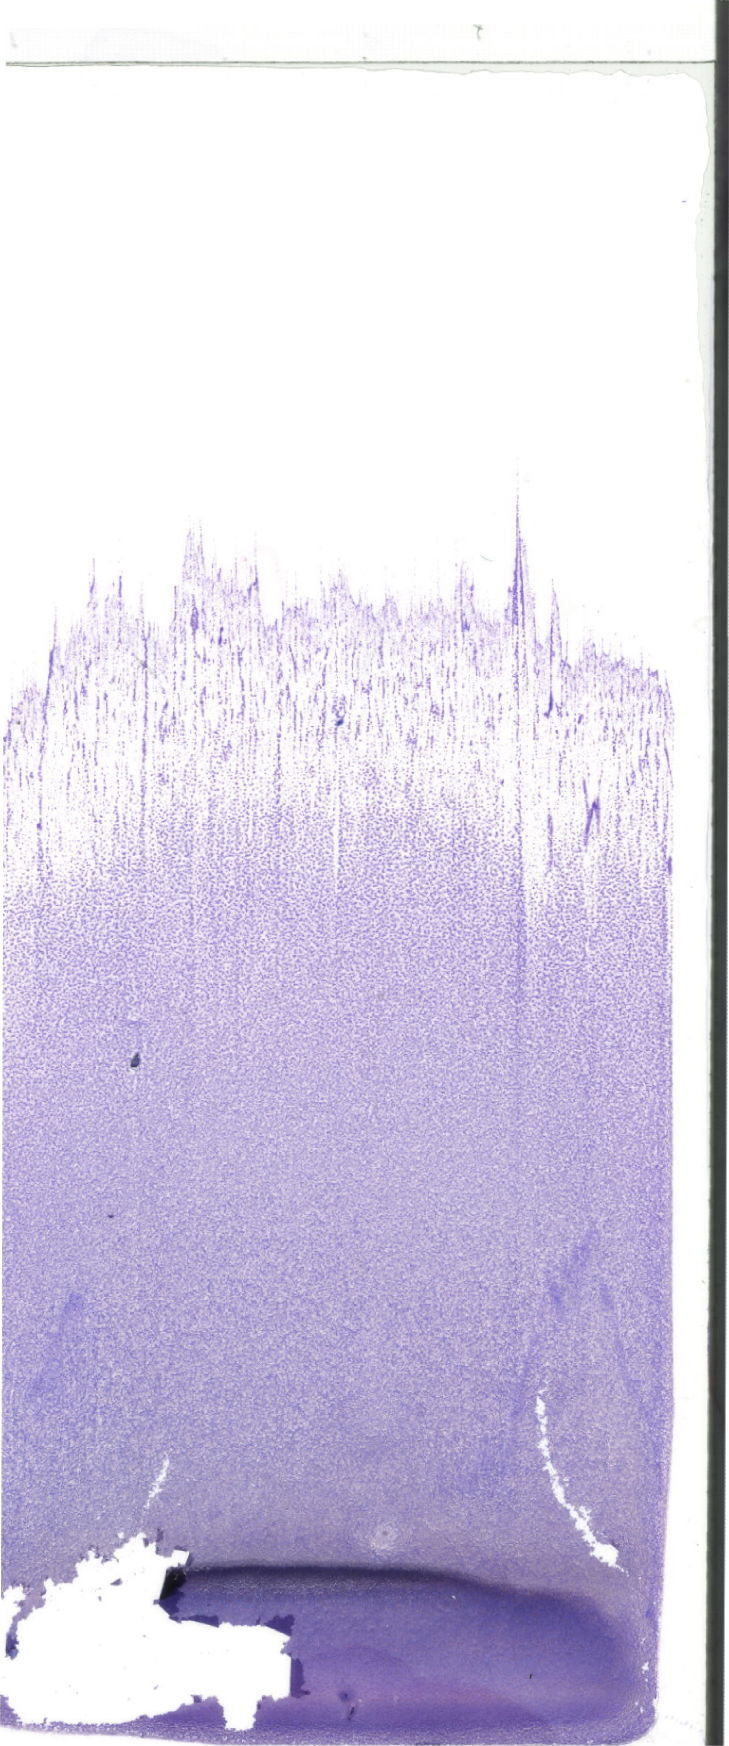
Whole-slide image of a May-Grünwald–Giemsa-stained bone marrow aspirate smear, shown as a low-resolution overview of the whole scanned area (about 20.7 x 49.5 mm). Female patient.
Diagnosis: Acute Myelomonocytic Leukemia.